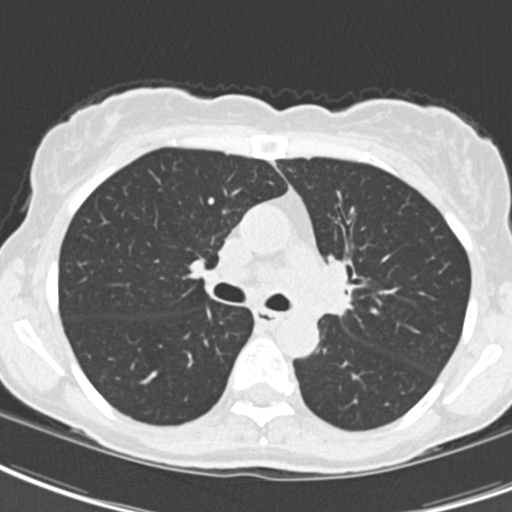
Low-dose screening chest CT, one axial slice. Slice 126 of 189 in the series (ordered by position). Reconstruction kernel B30f. Lung window (W 1500 / L -600 HU). 2 mm slice thickness. 512 × 512 image matrix, field of view 279 × 279 mm.
Annotated regions visible in this slice (outlined manually by an expert reader):
- lesion 2 (tumor, hilum of left lung): box from (x=324, y=262) to (x=351, y=315) px